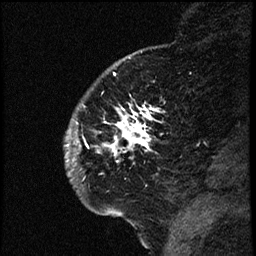
Breast MRI (dynamic contrast-enhanced), one sagittal slice. Slice 15 of 66 in the series (ordered by position). Dynamic contrast-enhanced study with each time point stored as its own series, time point 2 of 3 at this slice position (early post-contrast, ordered by acquisition time). 1.5 T. TE 4.2 ms, TR 17.6 ms. 2 mm slice thickness. 256 × 256 image matrix. Female patient. Case-level facts recorded for this patient, not image findings: setting: breast cancer imaged before/during neoadjuvant chemotherapy; receptor status: HER2-positive.
Structures marked on this image (semi-automatic segmentation, software-assisted and operator-edited):
- analysis volume of interest (the breast-tissue region the enhancement analysis was run in; not a lesion): bounding box <67,69,175,209> (left, top, right, bottom; pixels)
- tumour enhancement mask (voxels above the 100 % enhancement threshold inside the analysis volume of interest): <69,104,158,171>